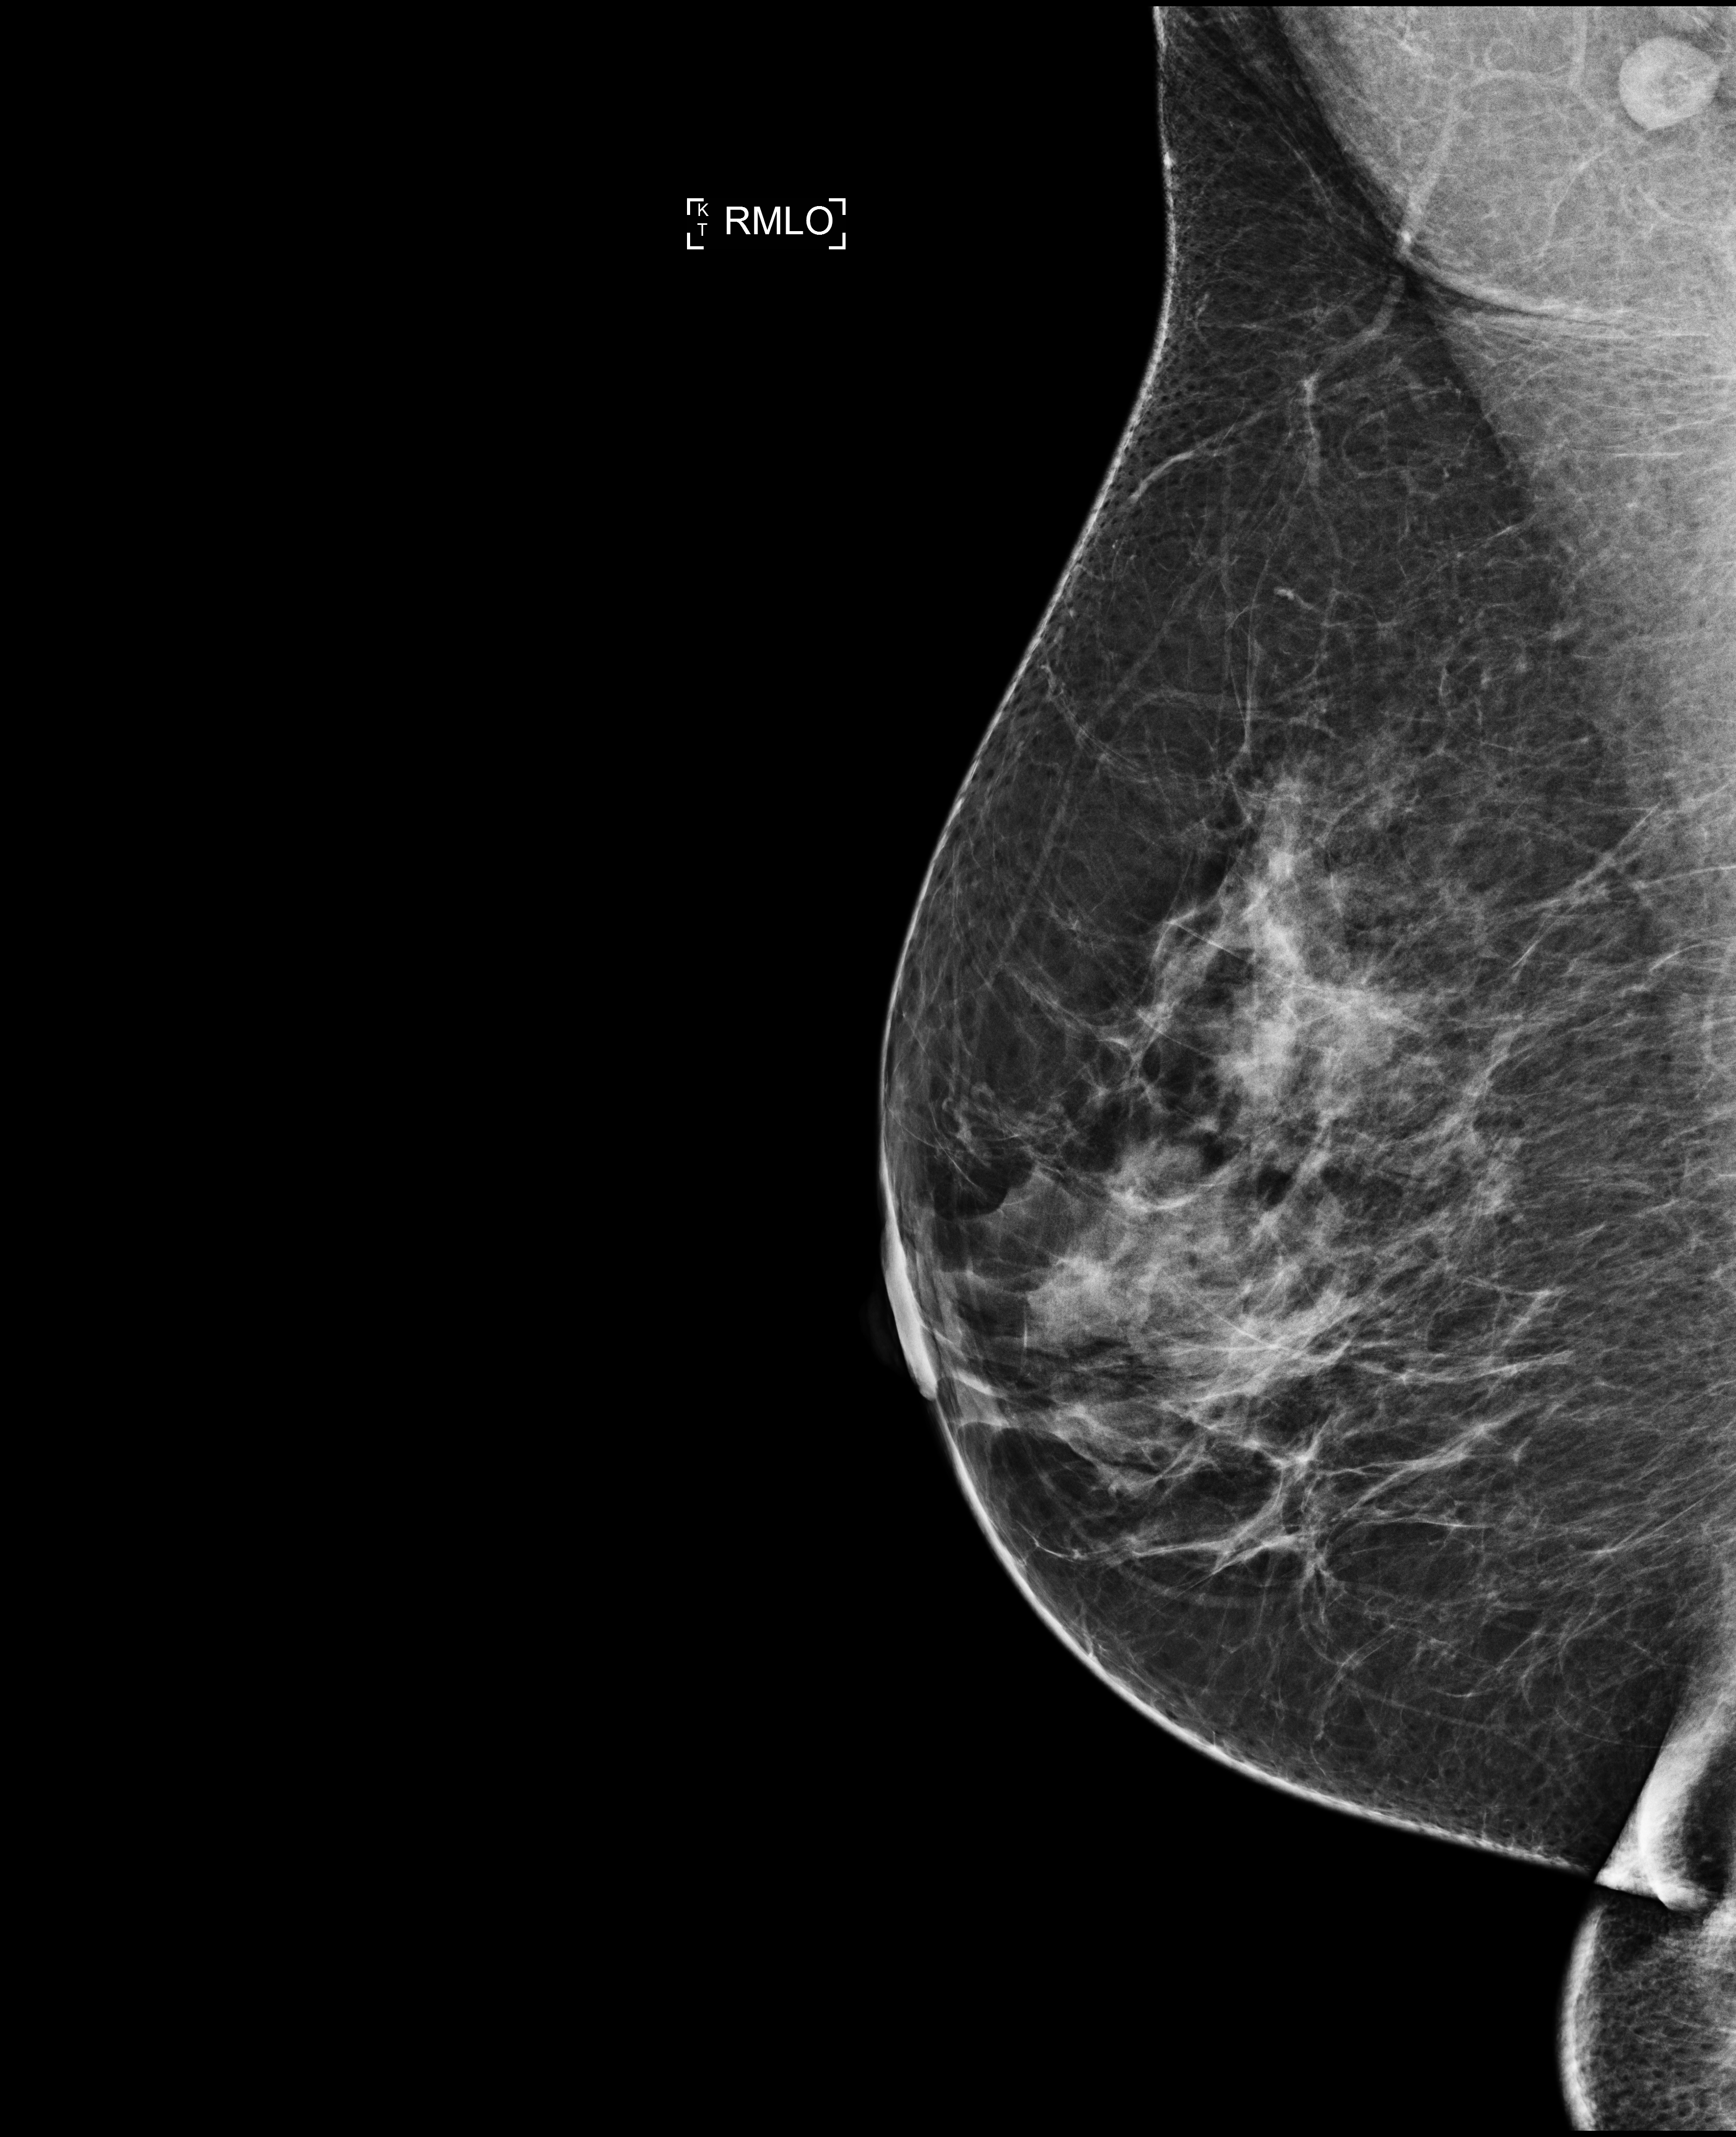
Screening examination. Female patient, age 54 years.
Image type: full-field digital mammogram. Breast: right. Projection: mediolateral oblique (MLO) view.